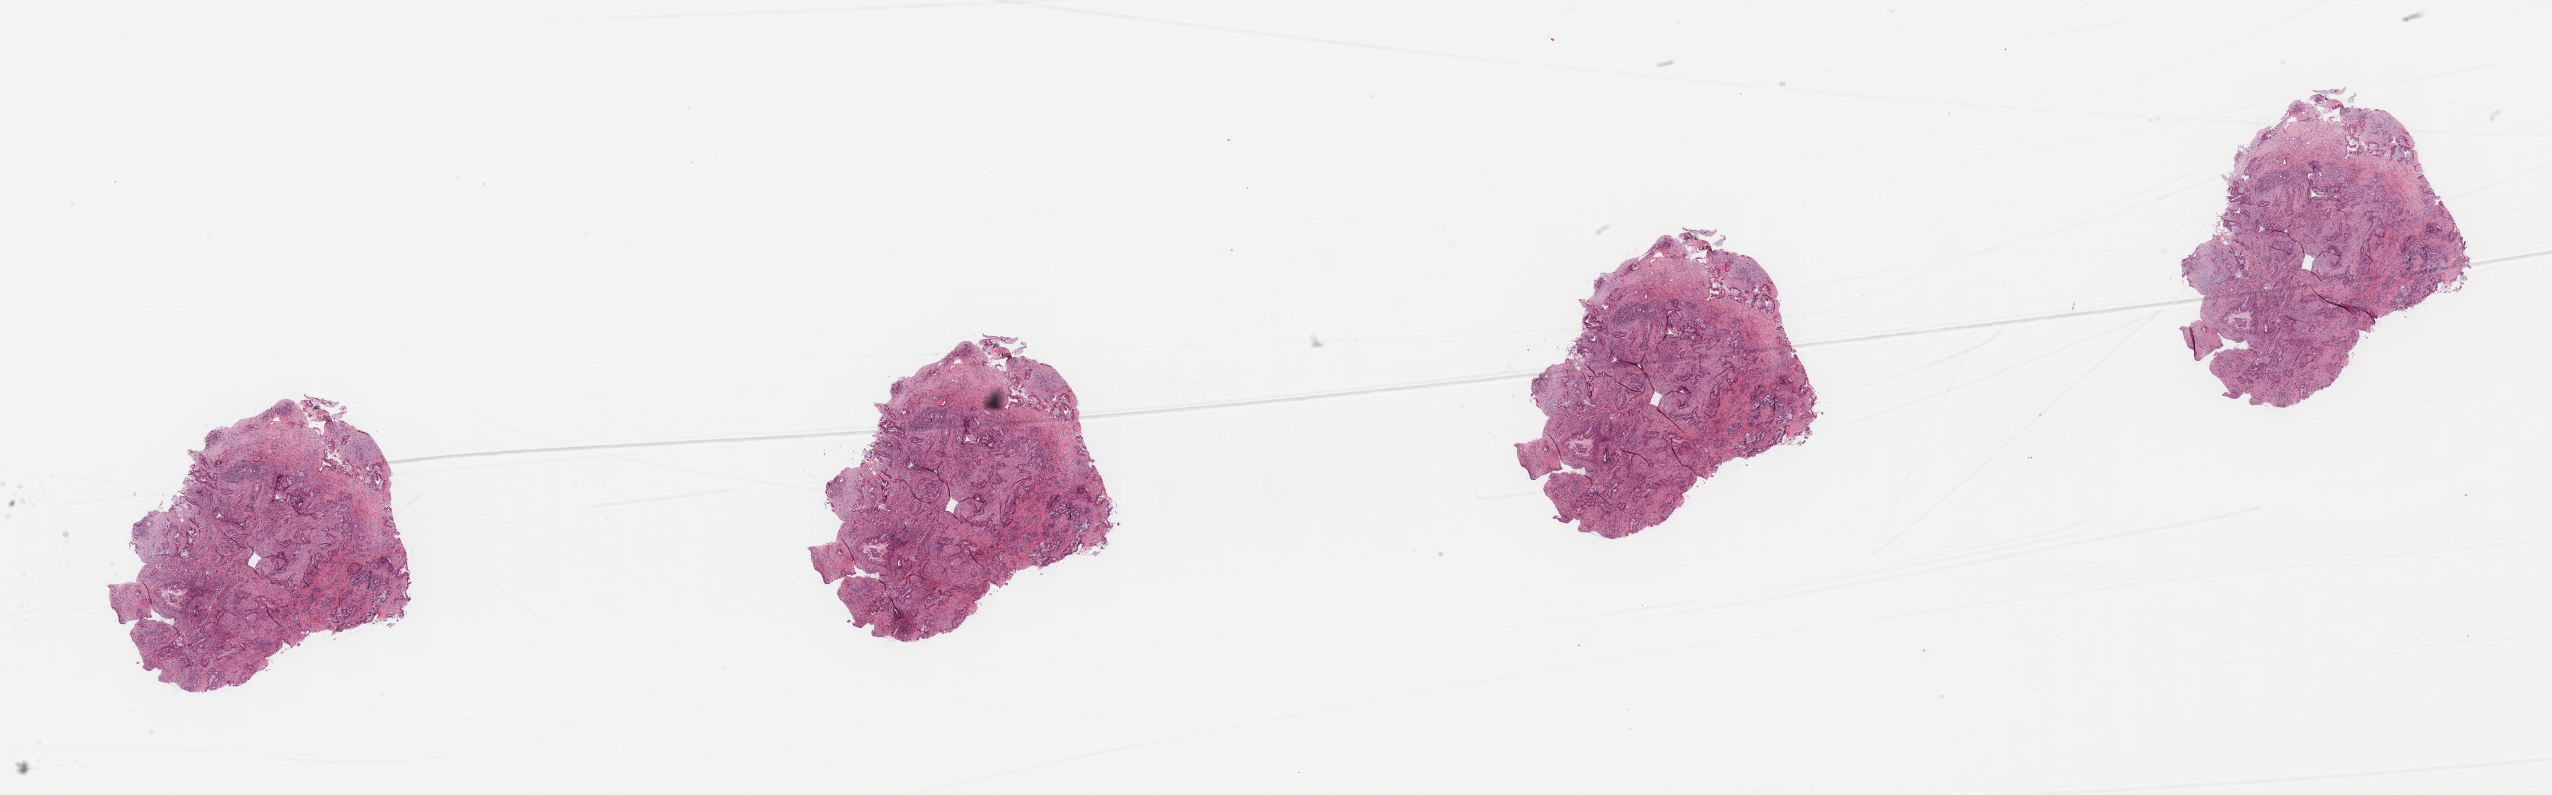
H&E whole-slide image — low-resolution overview of the scanned area, about 40.4 x 12.6 mm. Tumour tissue sample, pancreas. Female, 67 y/o. Histologic grade: G2 (moderately differentiated).
- diagnosis: Infiltrating duct carcinoma, NOS
- AJCC pathologic stage: III